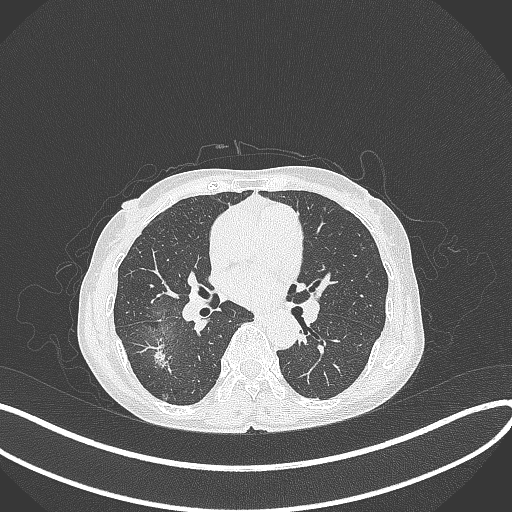
Chest CT, one axial slice; slice 204 of 371 in the series (ordered by position); lung window (W 1500 / L -600 HU); 1 mm slice thickness; 512 × 512 image matrix, field of view 400 × 400 mm. Female patient, age 69 years. Case-level facts recorded for this patient, not image findings: clinical TNM (as recorded): T1b N0 M0.
Outlined on this slice (bounding box drawn by a radiologist):
- lung tumour (recorded histology: adenocarcinoma): bounding box (x1, y1, x2, y2) in pixels: (144, 335, 175, 374)